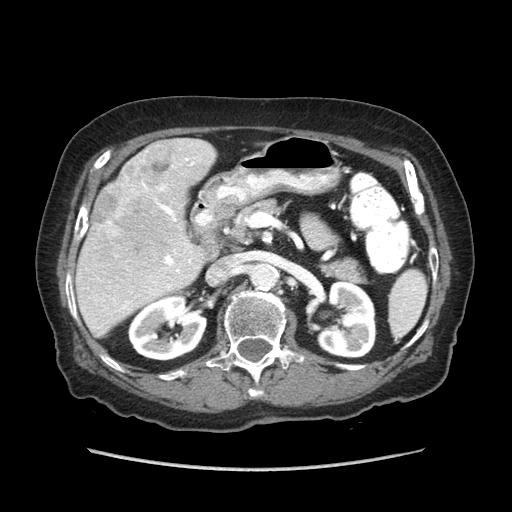
Contrast-enhanced abdominal CT (liver protocol), one axial slice. Slice 36 of 89 in the series (ordered by position). Reconstruction kernel STANDARD. Soft-tissue window (W 400 / L 40 HU). 2.5 mm slice thickness. 512 × 512 image matrix. From the clinical record (not read from this slice): diagnosis: hepatocellular carcinoma (patient treated with transarterial chemoembolisation; whether this scan precedes or follows treatment is not stated here); TNM stage (as recorded): Stage-IIIA; Child-Pugh class: A; tumour differentiation: well differentiated.
Annotated regions visible in this slice (semi-automatic segmentation, software-assisted and operator-edited):
- liver parenchyma outside the tumour (the mass and vessels are separate outlines, so this box may not span the whole liver): bounding box [x1, y1, x2, y2] px = [76, 138, 216, 336]
- mass: [91, 141, 175, 241]
- liver vessels: [122, 158, 195, 309]